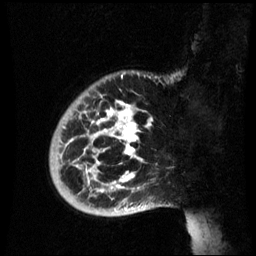
Breast MRI (dynamic contrast-enhanced), one sagittal slice. Slice 12 of 60 in the series (ordered by position). Dynamic contrast-enhanced series, image 2 of 3 at this slice position (ordered by acquisition). 1.5 T. TE 4.2 ms, TR 8.9 ms. 256 × 256 image matrix, field of view 220 × 220 mm. Female patient, age 35 years. Case-level facts recorded for this patient, not image findings: setting: breast cancer imaged before/during neoadjuvant chemotherapy; receptor status: HR-positive, HER2-negative.
Annotated regions visible in this slice (semi-automatic segmentation, software-assisted and operator-edited):
- analysis volume of interest (the breast-tissue region the enhancement analysis was run in; not a lesion): bounding box <49,74,164,217> (left, top, right, bottom; pixels)
- tumour enhancement mask (voxels above the 70 % enhancement threshold inside the analysis volume of interest): <67,100,142,193>